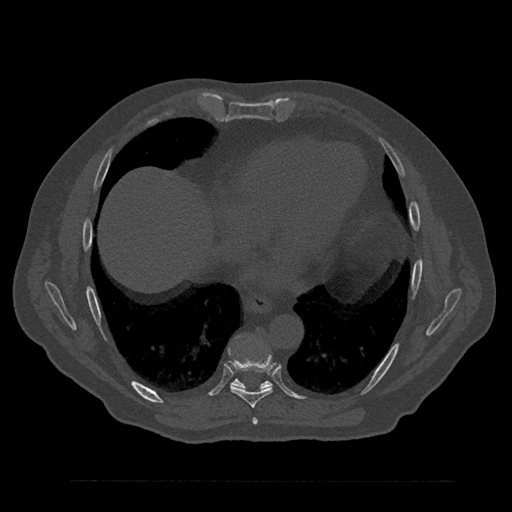
CT including the spine, one axial slice; slice 440 of 797 in the series (ordered by position); bone window (W 1800 / L 400 HU); 0.5 mm slice thickness; 512 × 512 image matrix. Patient: male, 61 years. From the clinical record (not read from this slice): primary cancer: prostate.
Outlined on this slice (semi-automatic segmentation, software-assisted and operator-edited):
- T7 vertebra: bounding box <252,418,258,425> (left, top, right, bottom; pixels)
- T8 vertebra: <230,352,276,408>
- T9 vertebra: <232,379,272,389>